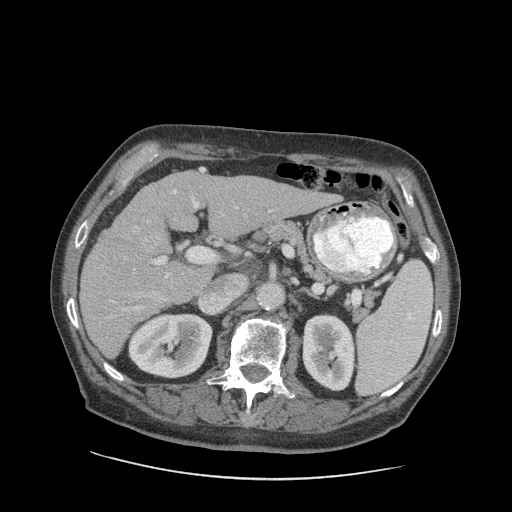
Contrast-enhanced abdominal CT (liver protocol), one axial slice; slice 48 of 89 in the series (ordered by position); soft-tissue window (W 400 / L 40 HU); 2.5 mm slice thickness; 512 × 512 image matrix. From the clinical record (not read from this slice): diagnosis: hepatocellular carcinoma (patient treated with transarterial chemoembolisation; whether this scan precedes or follows treatment is not stated here); TNM stage (as recorded): Stage-I; Child-Pugh class: A; tumour differentiation: moderately differentiated; tumour size: 4.6 cm.
Structures marked on this image (semi-automatically segmented with operator editing):
- liver parenchyma outside the tumour (the mass and vessels are separate outlines, so this box may not span the whole liver): bounding box [x1, y1, x2, y2] px = [79, 168, 337, 358]
- mass: [136, 222, 171, 258]
- liver vessels: [110, 169, 275, 318]